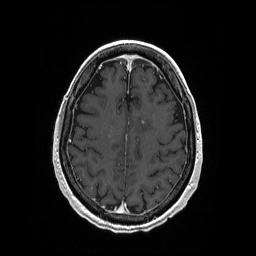
Brain MRI from a brain-tumour surgery series, one axial slice. Position 69 of 208 along the scan axis. T1-weighted post-contrast. 256 × 256 image matrix, field of view 256 × 256 mm. Case-level facts recorded for this patient, not image findings: histopathology: Primary diffuse large B-cell lymphoma; tumour location: Left Corpus Callosum (Frontal).
Annotated regions visible in this slice (manually delineated by an expert):
- tumour: box from (x=141, y=121) to (x=145, y=124) px